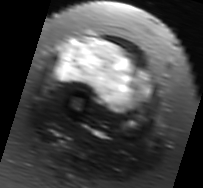
MRI of an extremity soft-tissue mass, one axial slice. Position 27 of 91 along the scan axis. T2-weighted fat-saturated. MR volume resampled by the dataset authors to the PET/CT grid (not the native acquisition matrix). 3.27 mm slice thickness. 203 × 188 image matrix, field of view 198 × 184 mm. Female patient. Case-level facts recorded for this patient, not image findings: histological type: malignant solitary fibrous tumor; grade: intermediate; site of the primary tumour: right thigh.
Annotated regions visible in this slice (expert contour drawn on MRI and transferred to this co-registered scan by the dataset authors):
- gross tumour volume including surrounding oedema: bounding box [x1, y1, x2, y2] px = [53, 35, 155, 116]
- gross tumour volume (mass): [56, 40, 146, 107]